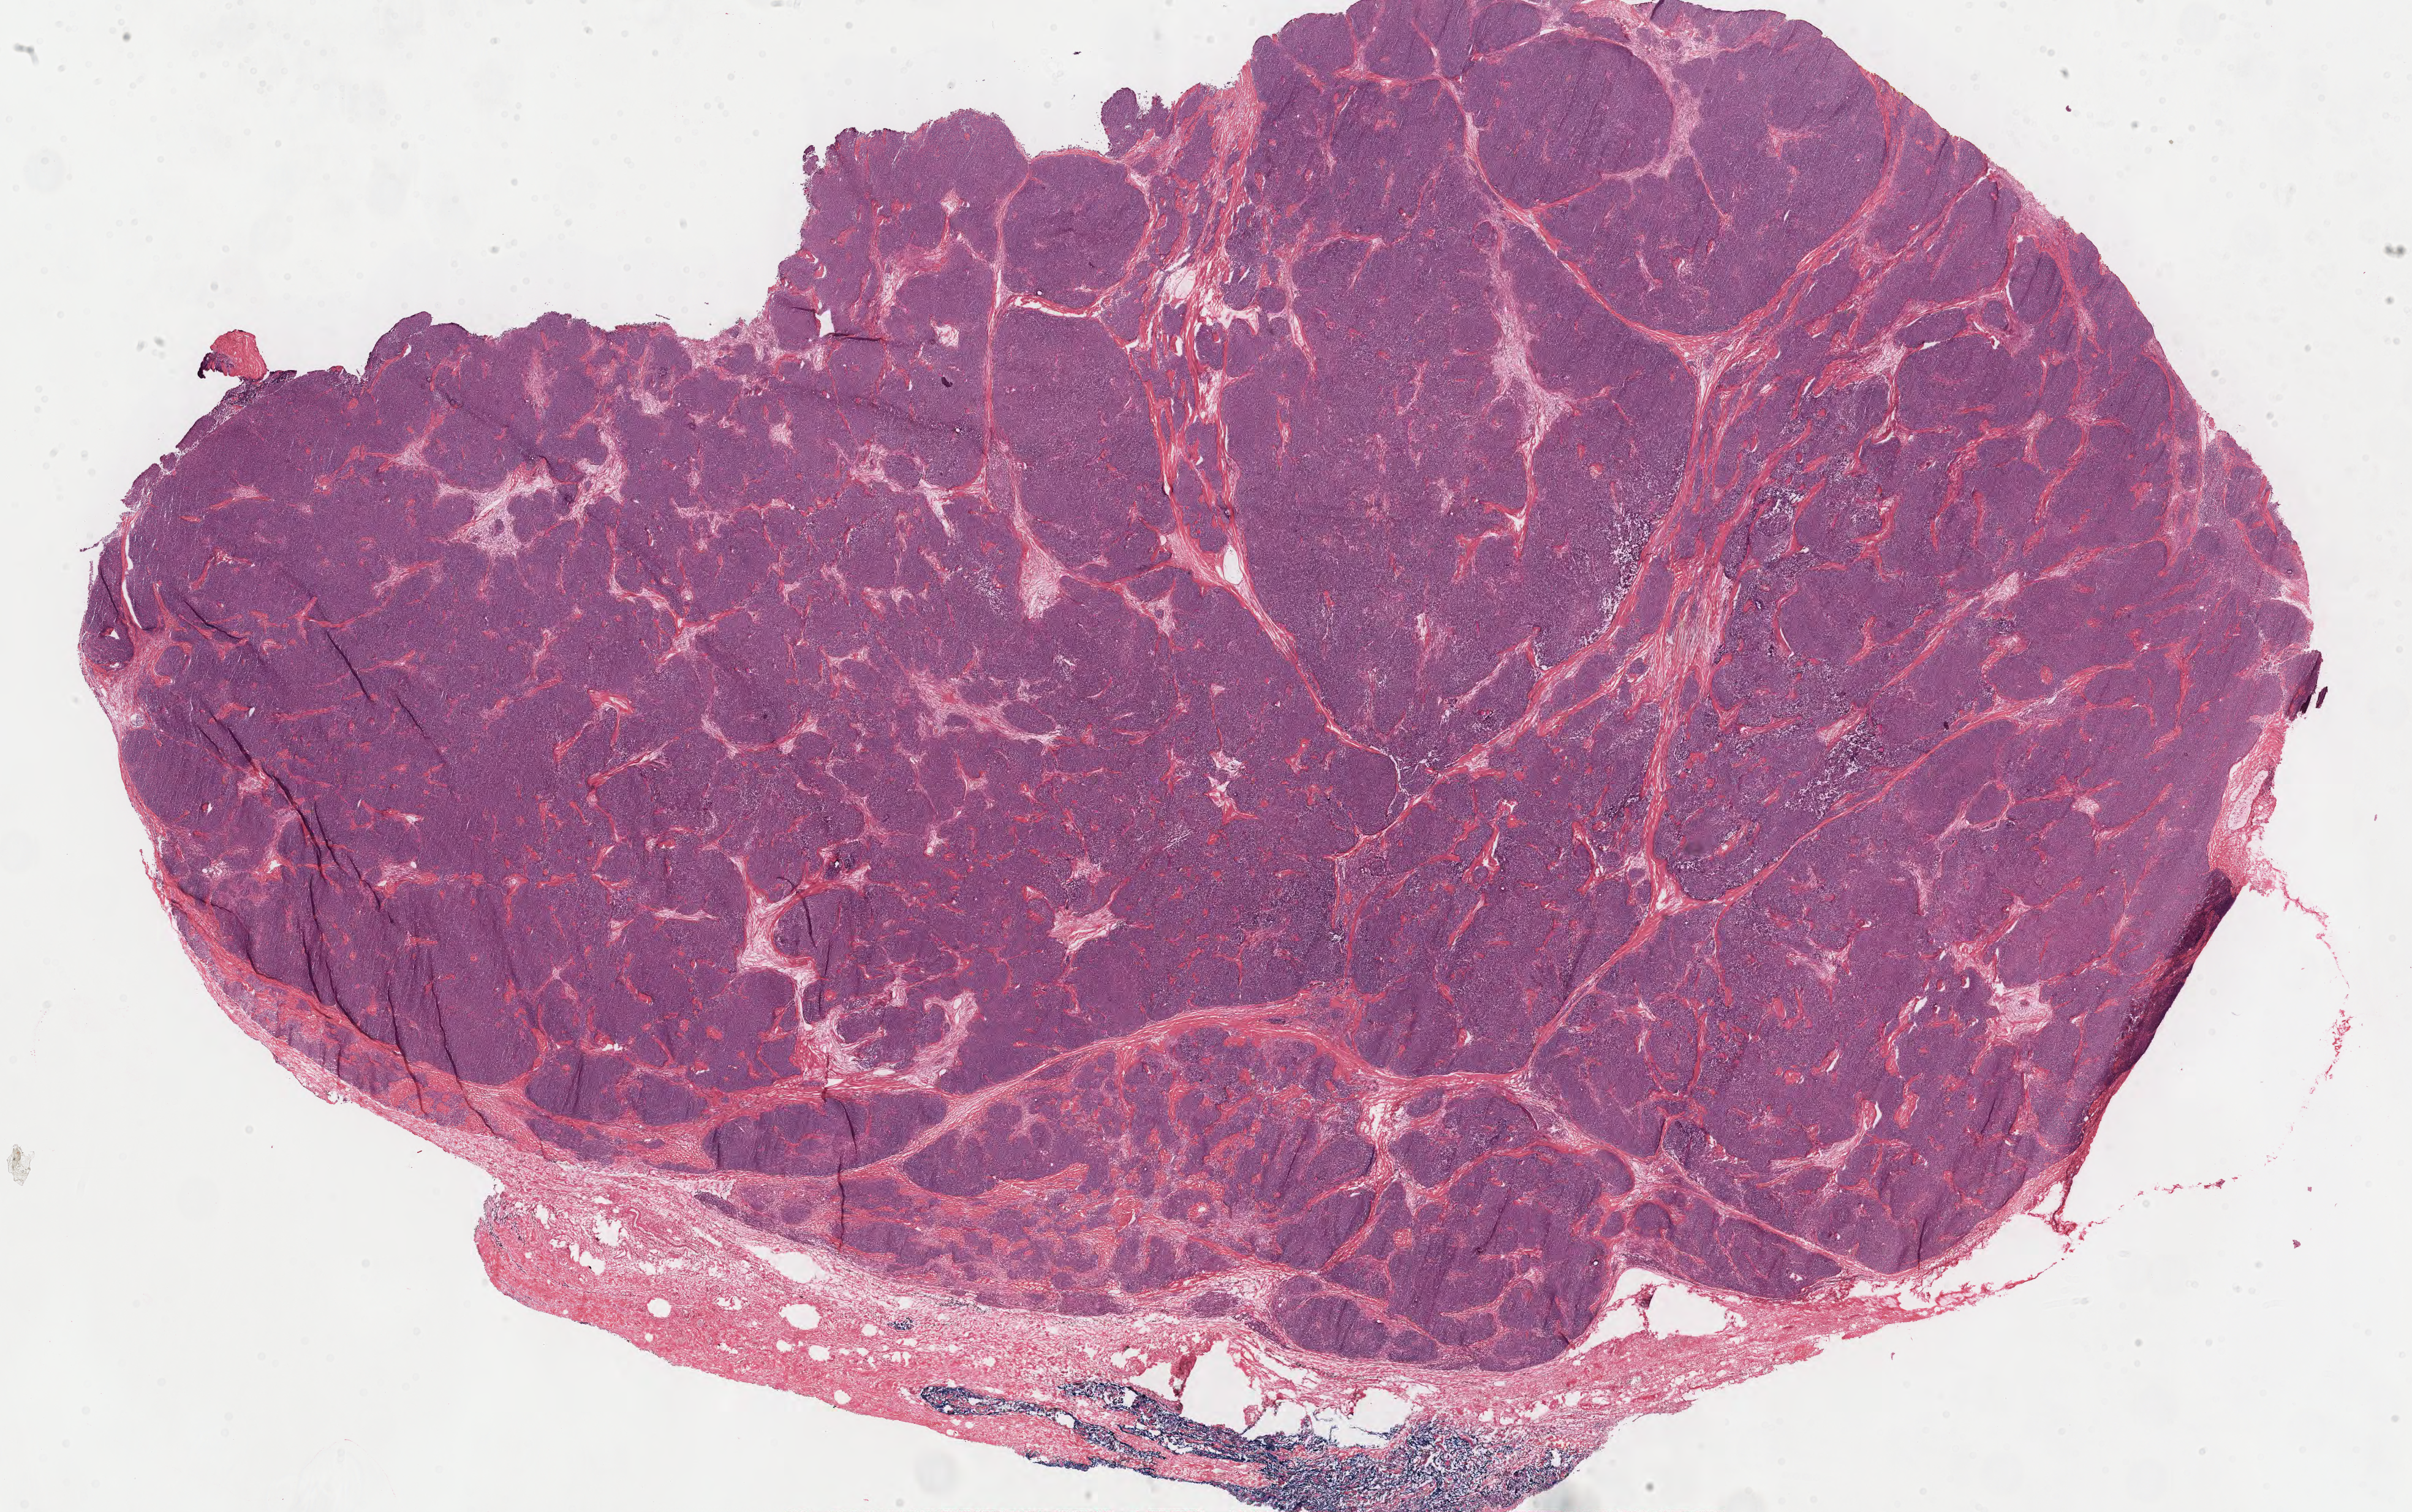
Digitized H&E-stained tissue section (whole slide), a low-resolution overview of the entire scanned area, about 31.2 x 19.6 mm (acquisition: 40x scan). Formalin-fixed paraffin-embedded (FFPE) diagnostic section. Thymus, primary tumour sample. Patient: female, age at initial diagnosis 50 years.
- pathologic diagnosis: Thymoma, type AB, malignant